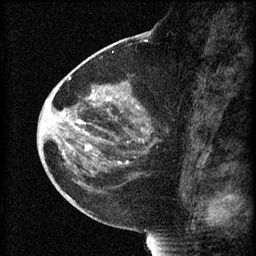
Breast MRI (dynamic contrast-enhanced), one sagittal slice; slice 30 of 60 in the series (ordered by position); 3 images stored at this slice position (order not interpretable as contrast timing); 1.5 T; TE 4.2 ms, TR 8.2 ms; 256 × 256 image matrix. Female patient, age 44 years.
Annotated regions visible in this slice (semi-automatically segmented with operator editing):
- analysis volume of interest (the breast-tissue region the enhancement analysis was run in; not a lesion): bounding box (x1, y1, x2, y2) in pixels: (73, 82, 169, 165)
- tumour enhancement mask (voxels above the 70 % enhancement threshold inside the analysis volume of interest): (74, 90, 145, 165)